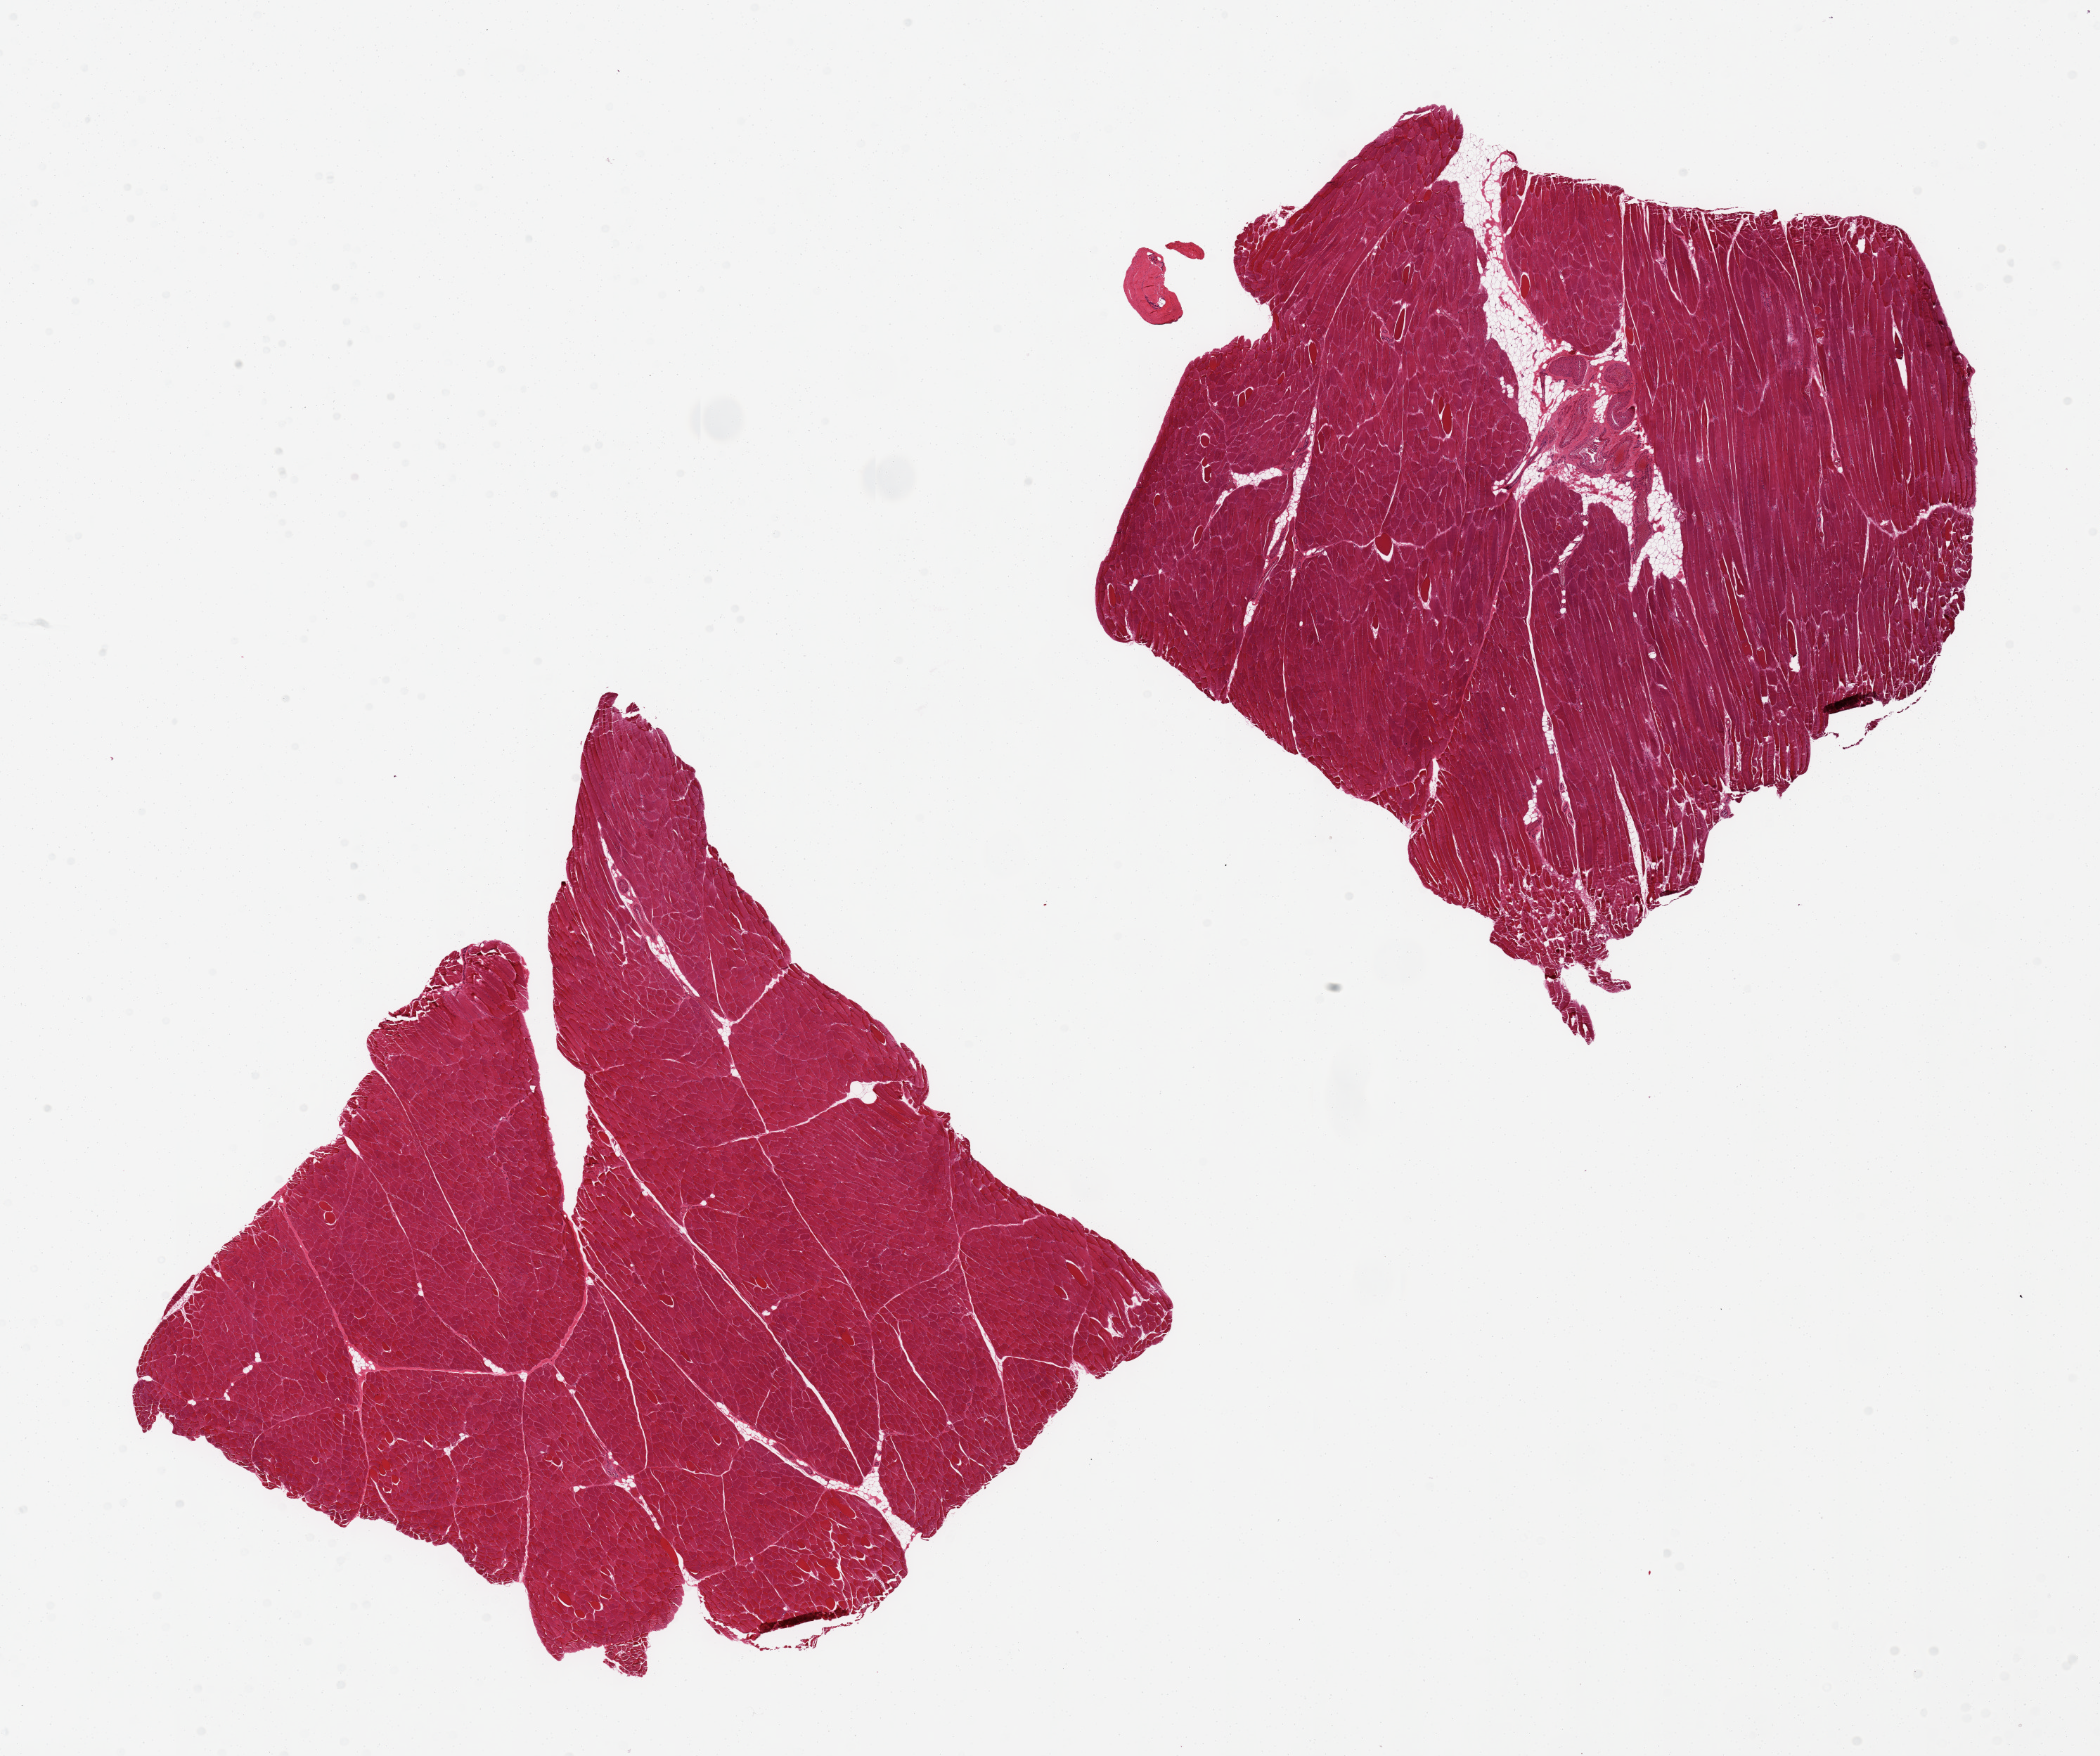
Haematoxylin and eosin whole-slide image — a low-resolution overview of the entire scanned area, about 23.6 x 19.8 mm (slide scanned at 20x), PAXgene-fixed paraffin-embedded (PFPE) section, sampled site (target tissue): skeletal muscle, donor tissue sample. Donor sex: male.
Pathologist's review note for this sample: 2 pieces; 1 has internal 10% fat and vascular tissue.